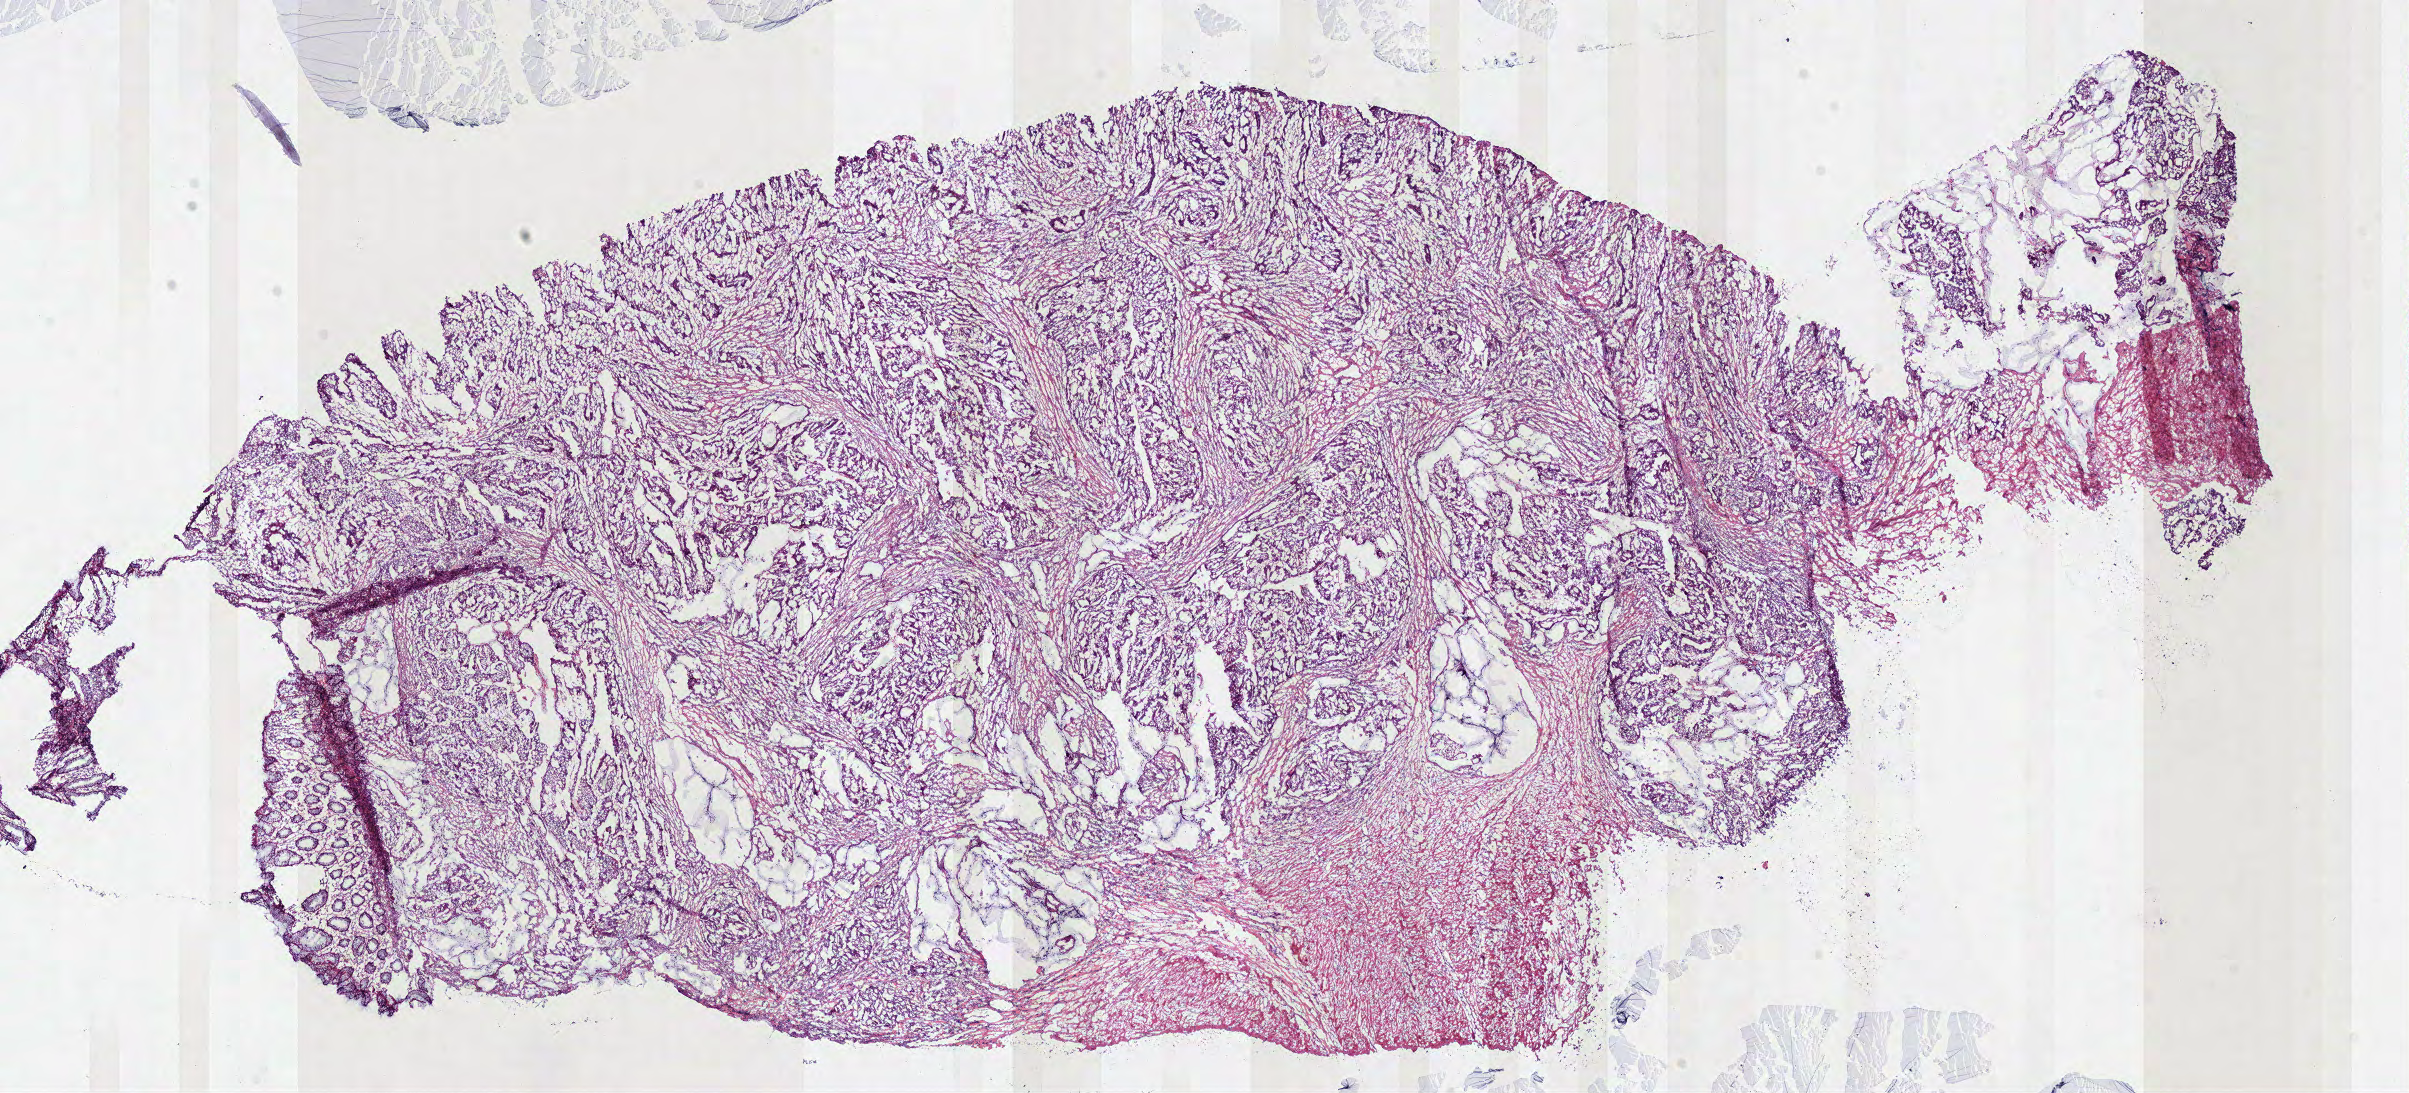
Digitized Hematoxylin and eosin (H&E) stained tissue section (whole slide) — whole scanned area (about 19.0 x 8.6 mm, slide scanned at 40x) shown as a low-resolution overview, frozen section from the top of the tissue portion, sample: primary tumour, rectum. Patient: female, age at initial diagnosis 60 years. Composition of this section per pathologist review: tumour cells 87%, tumour nuclei 80%, normal cells 3%, stromal cells 10%, necrosis 0%.
* AJCC pathologic stage: IIA (7th edition)
* lymph nodes positive (case pathology): 0 of 8 examined
* diagnosis: Adenocarcinoma, NOS